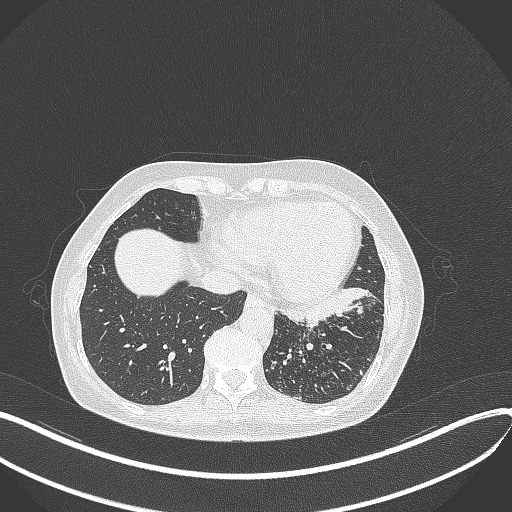
Chest CT, one axial slice; position 116 of 429 along the scan axis; 100 kVp; lung window (W 1500 / L -600 HU); 1 mm slice thickness; 512 × 512 image matrix, field of view 400 × 400 mm. Patient: female, 63 years. Case-level facts recorded for this patient, not image findings: clinical TNM (as recorded): T1b N0 M0.
Annotated regions visible in this slice (rectangle marked by the reading radiologist):
- lung tumour (recorded histology: adenocarcinoma): box from (x=285, y=282) to (x=375, y=333) px